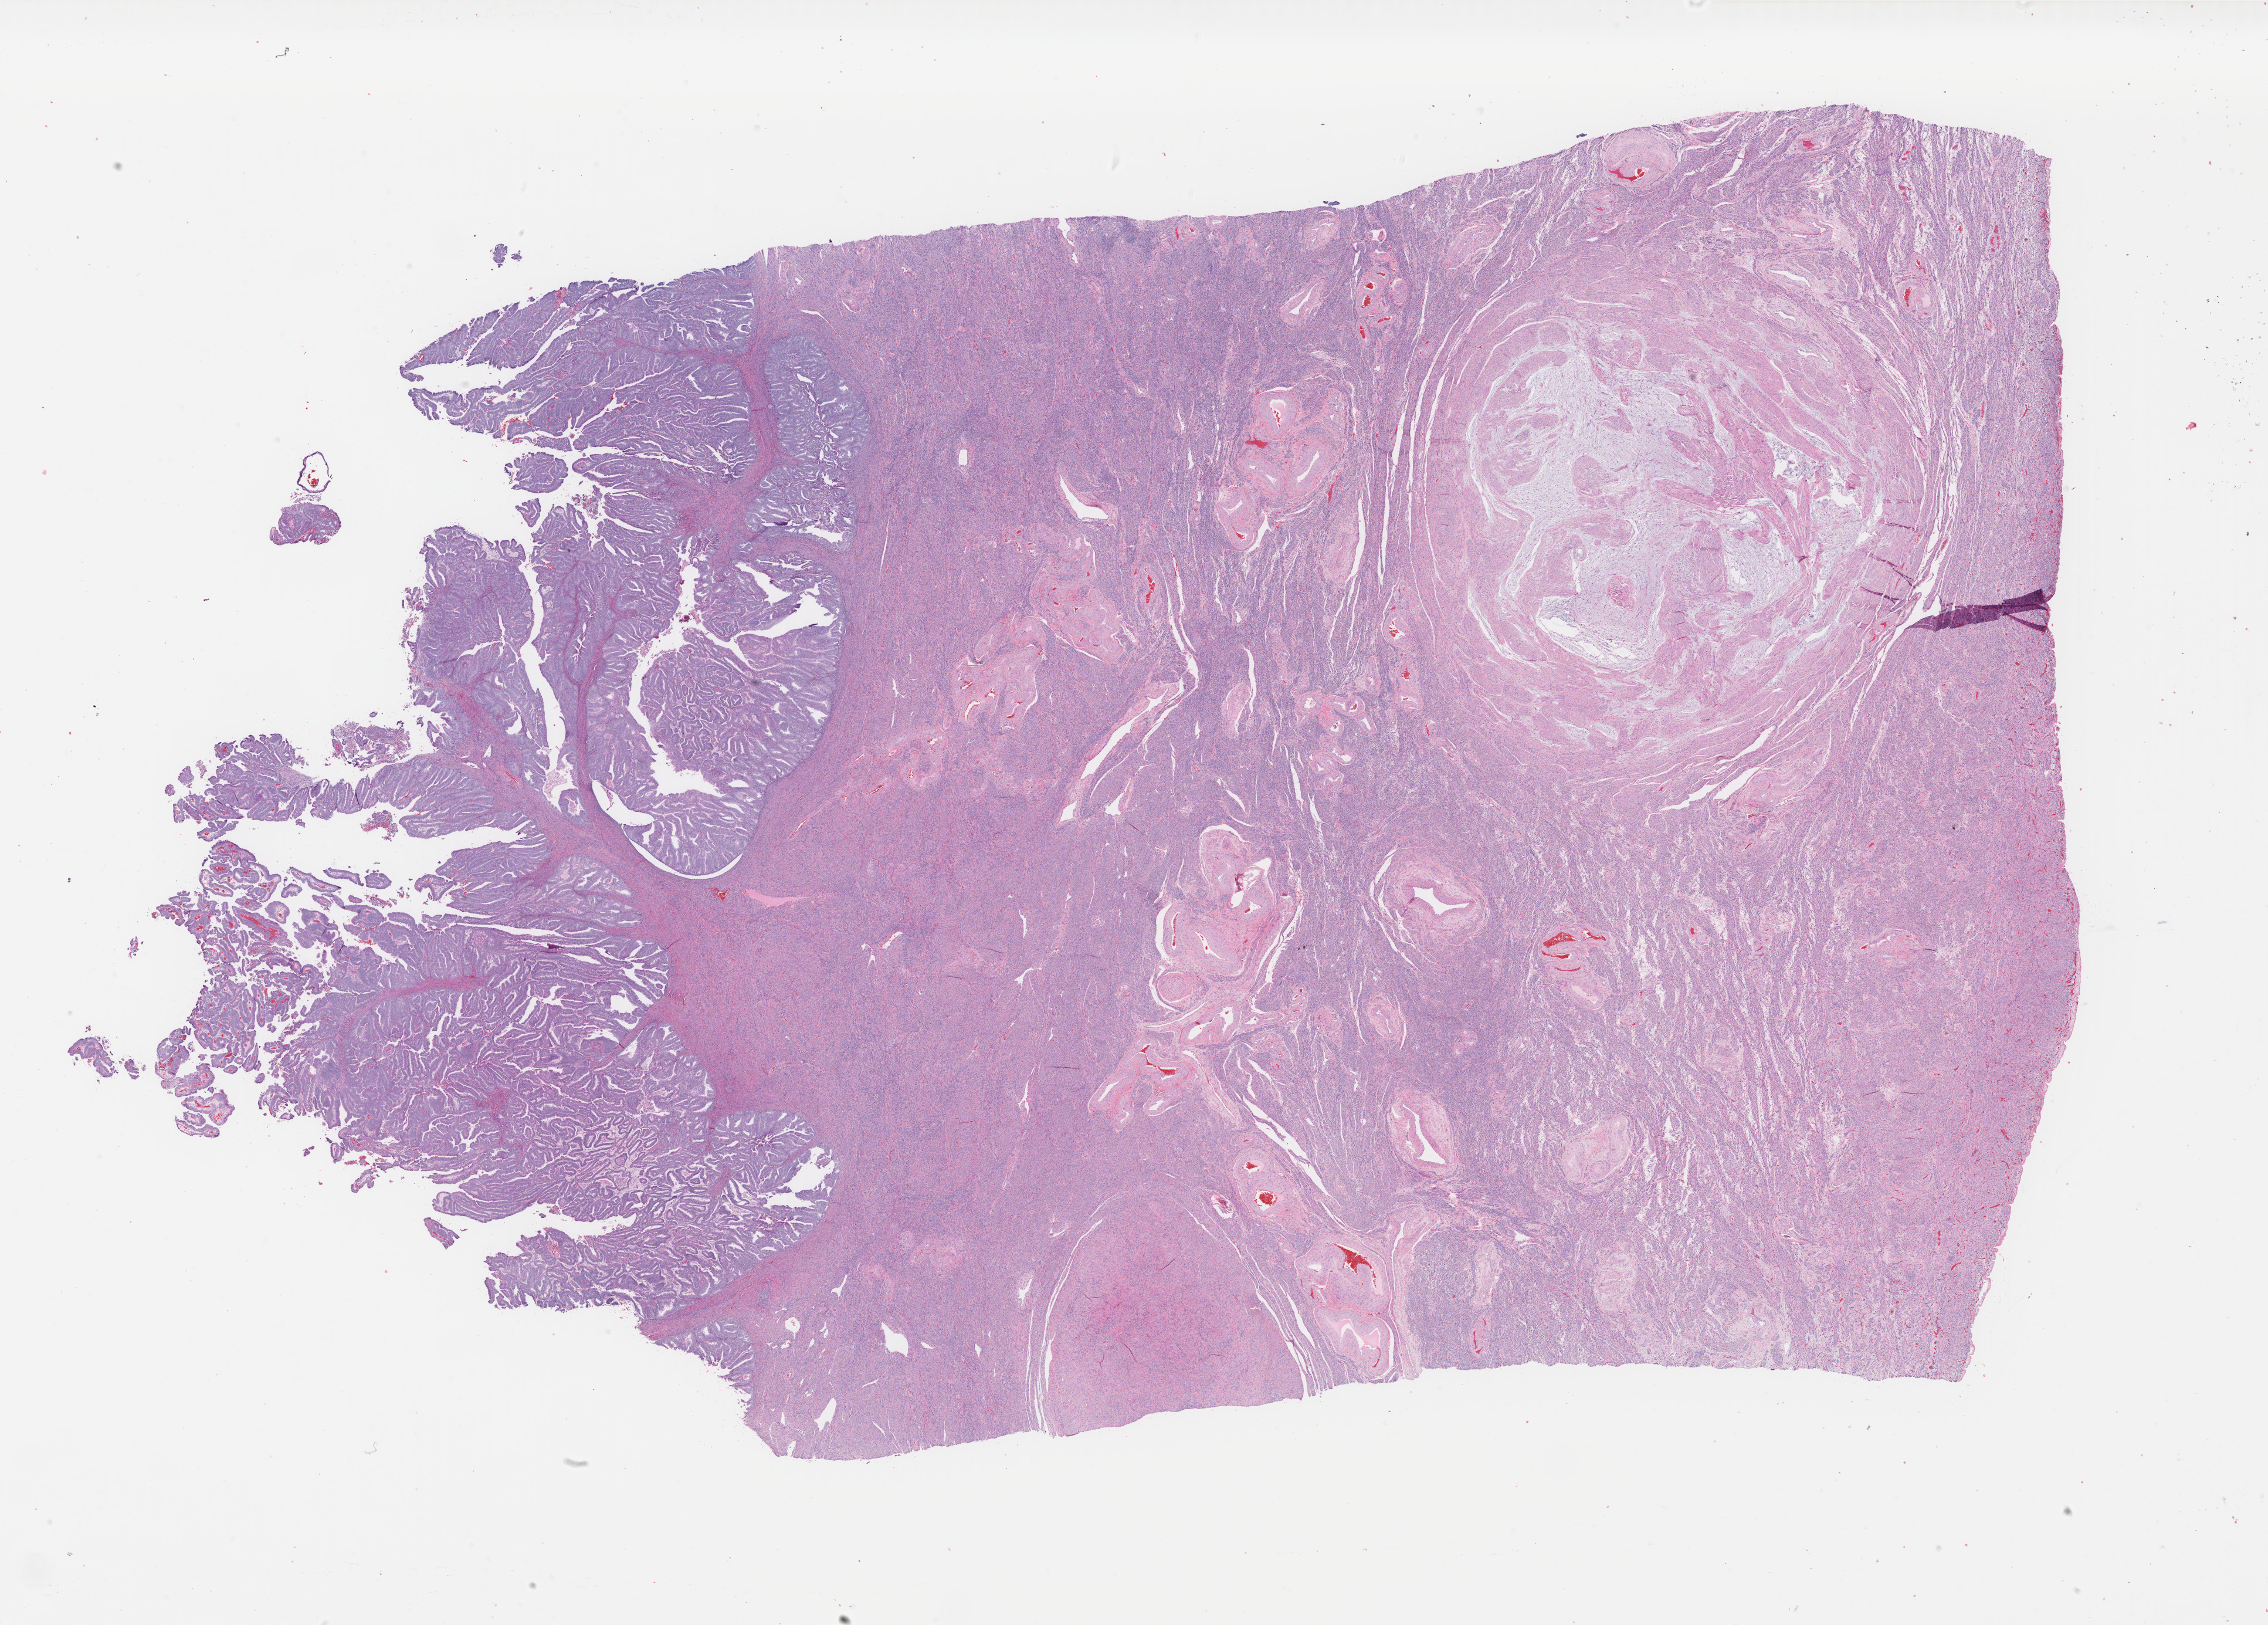
Digitized H&E-stained tissue section (whole slide), low-resolution overview of the scanned area, about 30.7 x 22.0 mm (slide scanned at 40x). Formalin-fixed paraffin-embedded (FFPE) diagnostic section. Sample: primary tumour, uterus. Female patient; age at initial diagnosis 69 years. Histologic grade: G1 (well differentiated).
Diagnosis: Endometrioid adenocarcinoma, NOS. FIGO stage: IA.